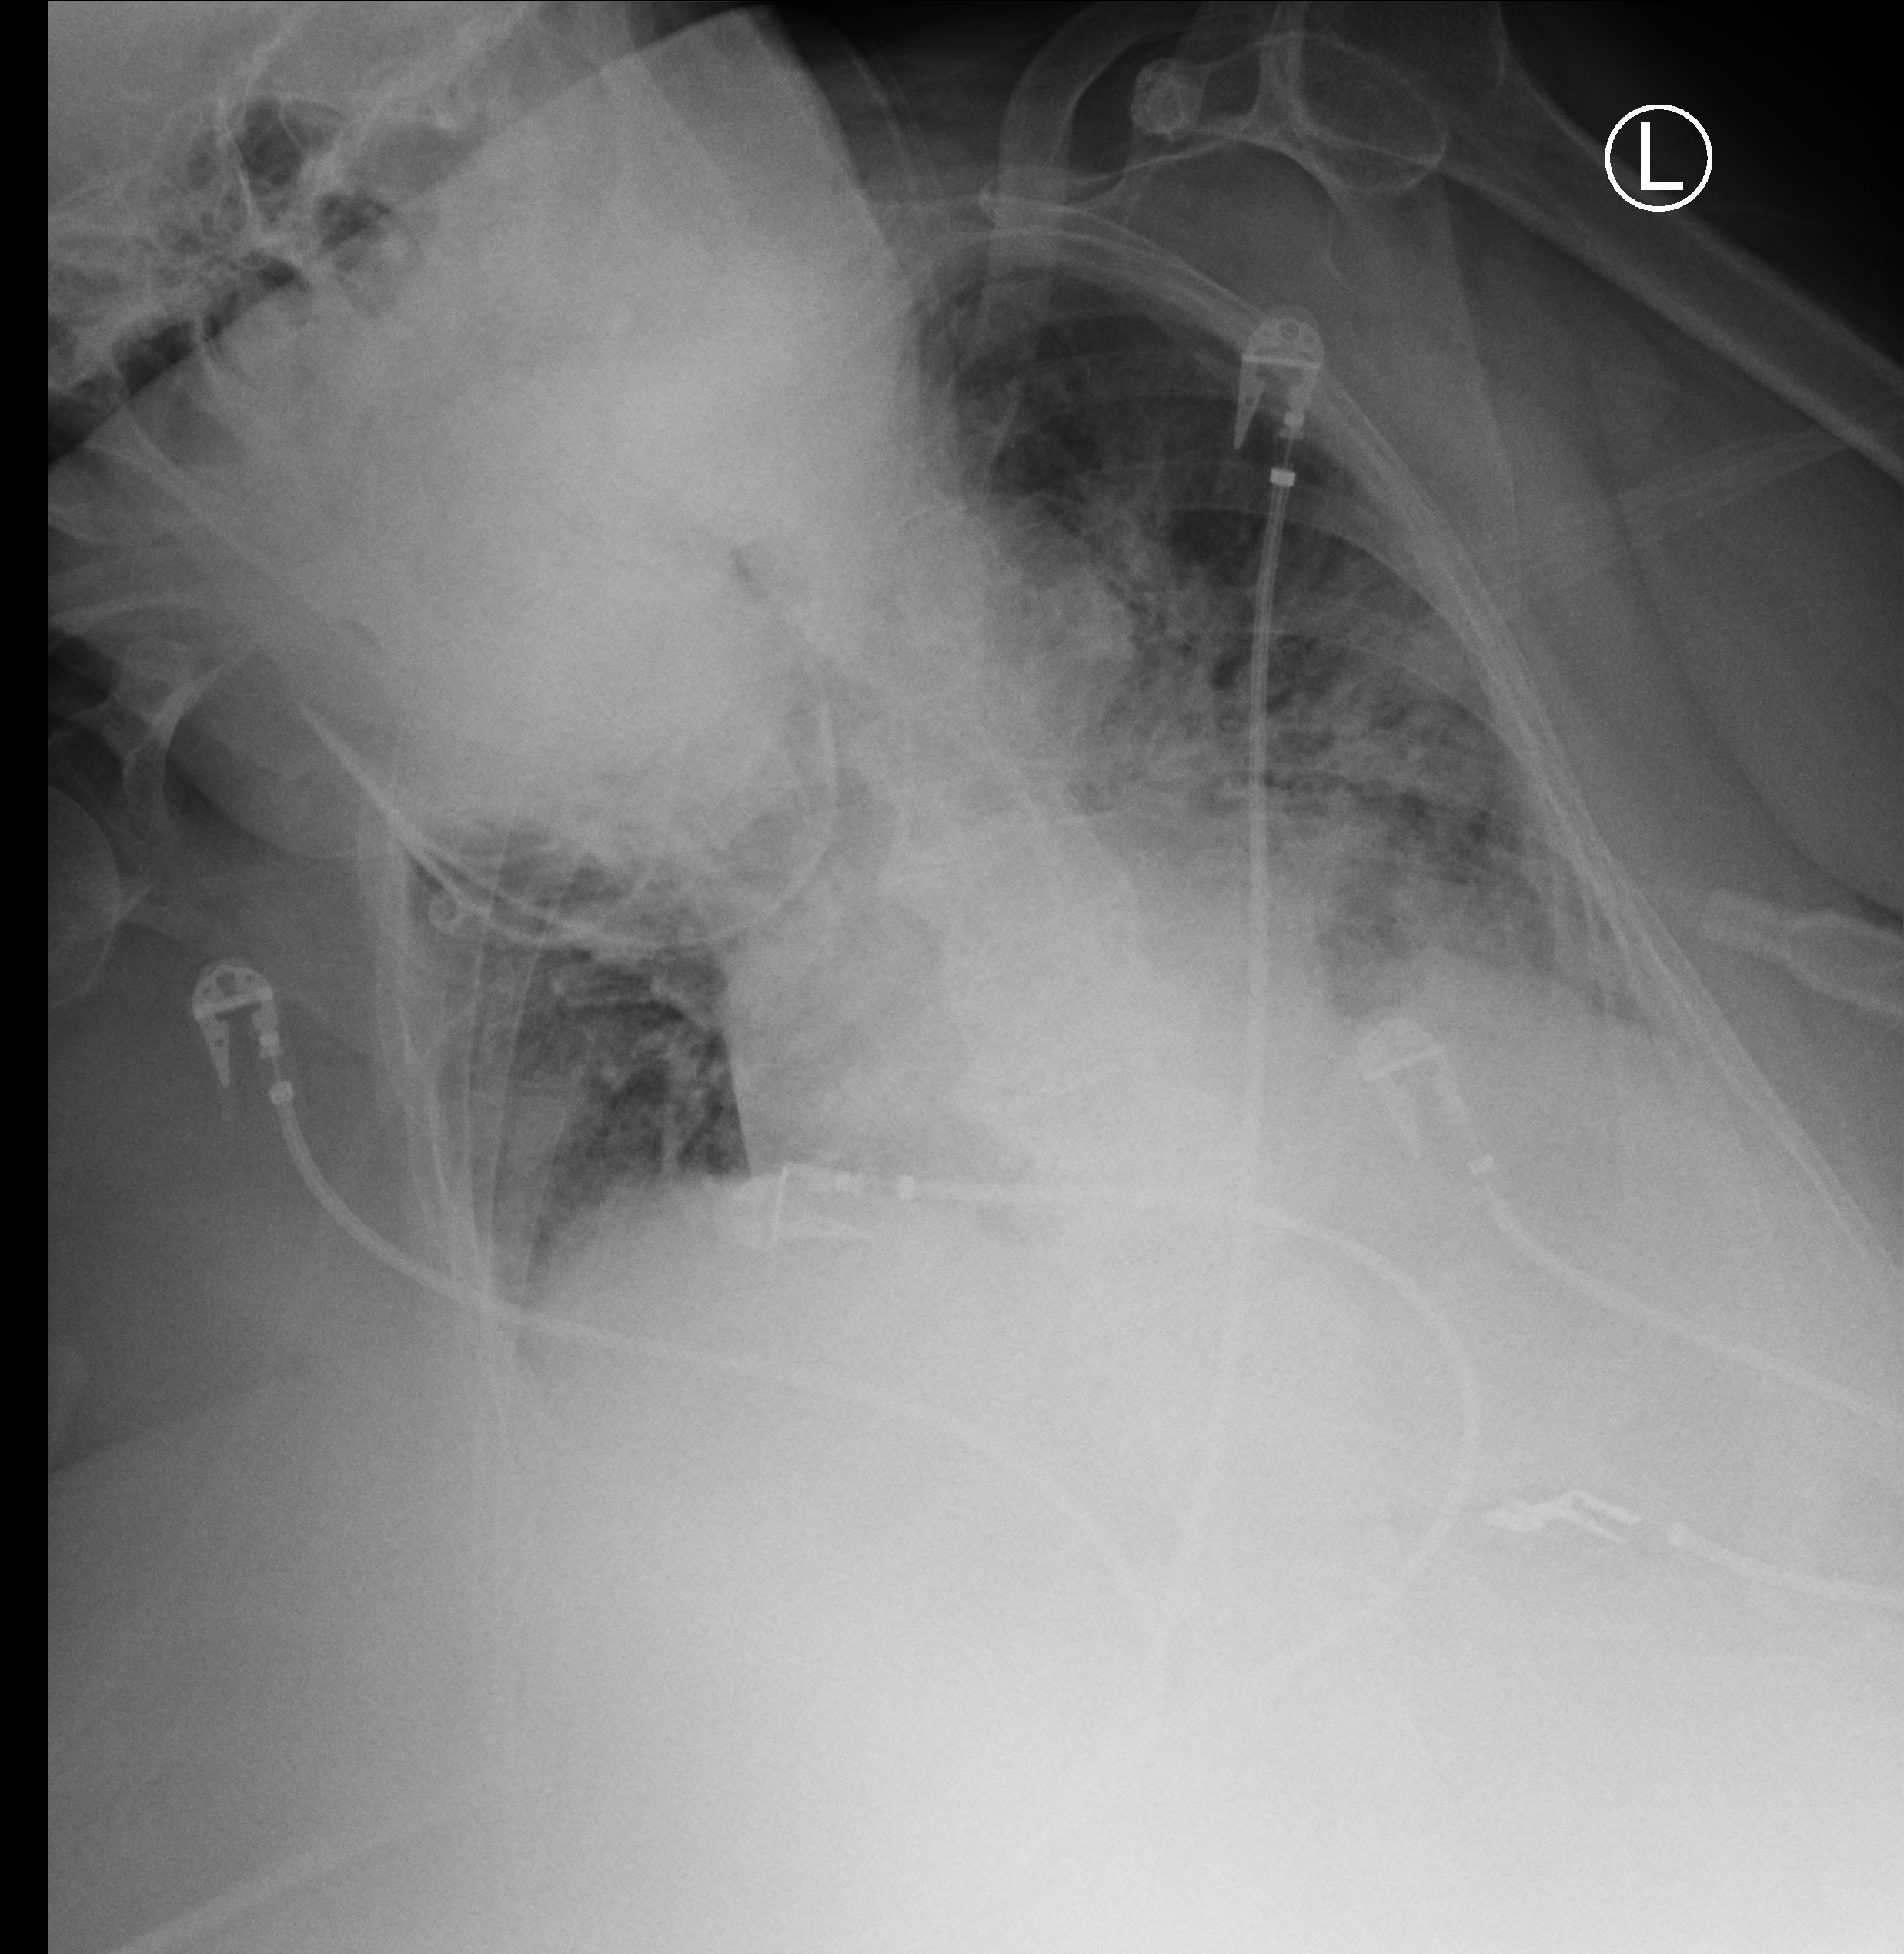
Chest X-ray (portable), anteroposterior (AP) projection. Patient hospitalised with COVID-19; female, aged 75–90 years.
From the hospital-stay record, not from the radiograph (when in the stay this image was taken is not recorded): admitted to intensive care during this hospital stay: no.